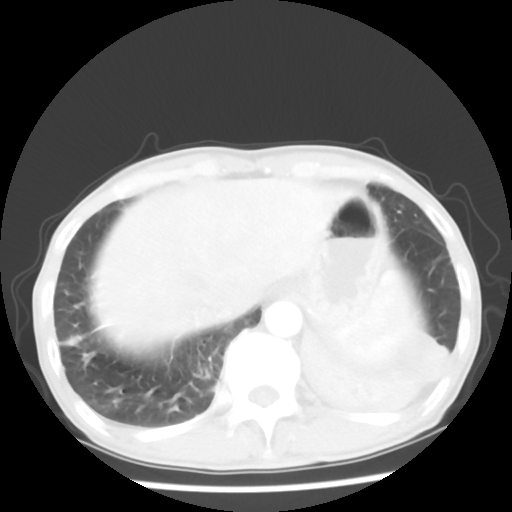
Chest CT, one axial slice. Slice 11 of 64 in the series (ordered by position). Reconstruction kernel STANDARD. 120 kVp. Lung window (W 1500 / L -600 HU). 5 mm slice thickness. 512 × 512 image matrix, field of view 313 × 313 mm. Male patient, age 68 years. From the clinical record (not read from this slice): clinical TNM (as recorded): T4 N0 M0.
Outlined on this slice (bounding box drawn by a radiologist):
- lung tumour (recorded histology: squamous cell carcinoma): bounding box <295,325,456,447> (left, top, right, bottom; pixels)